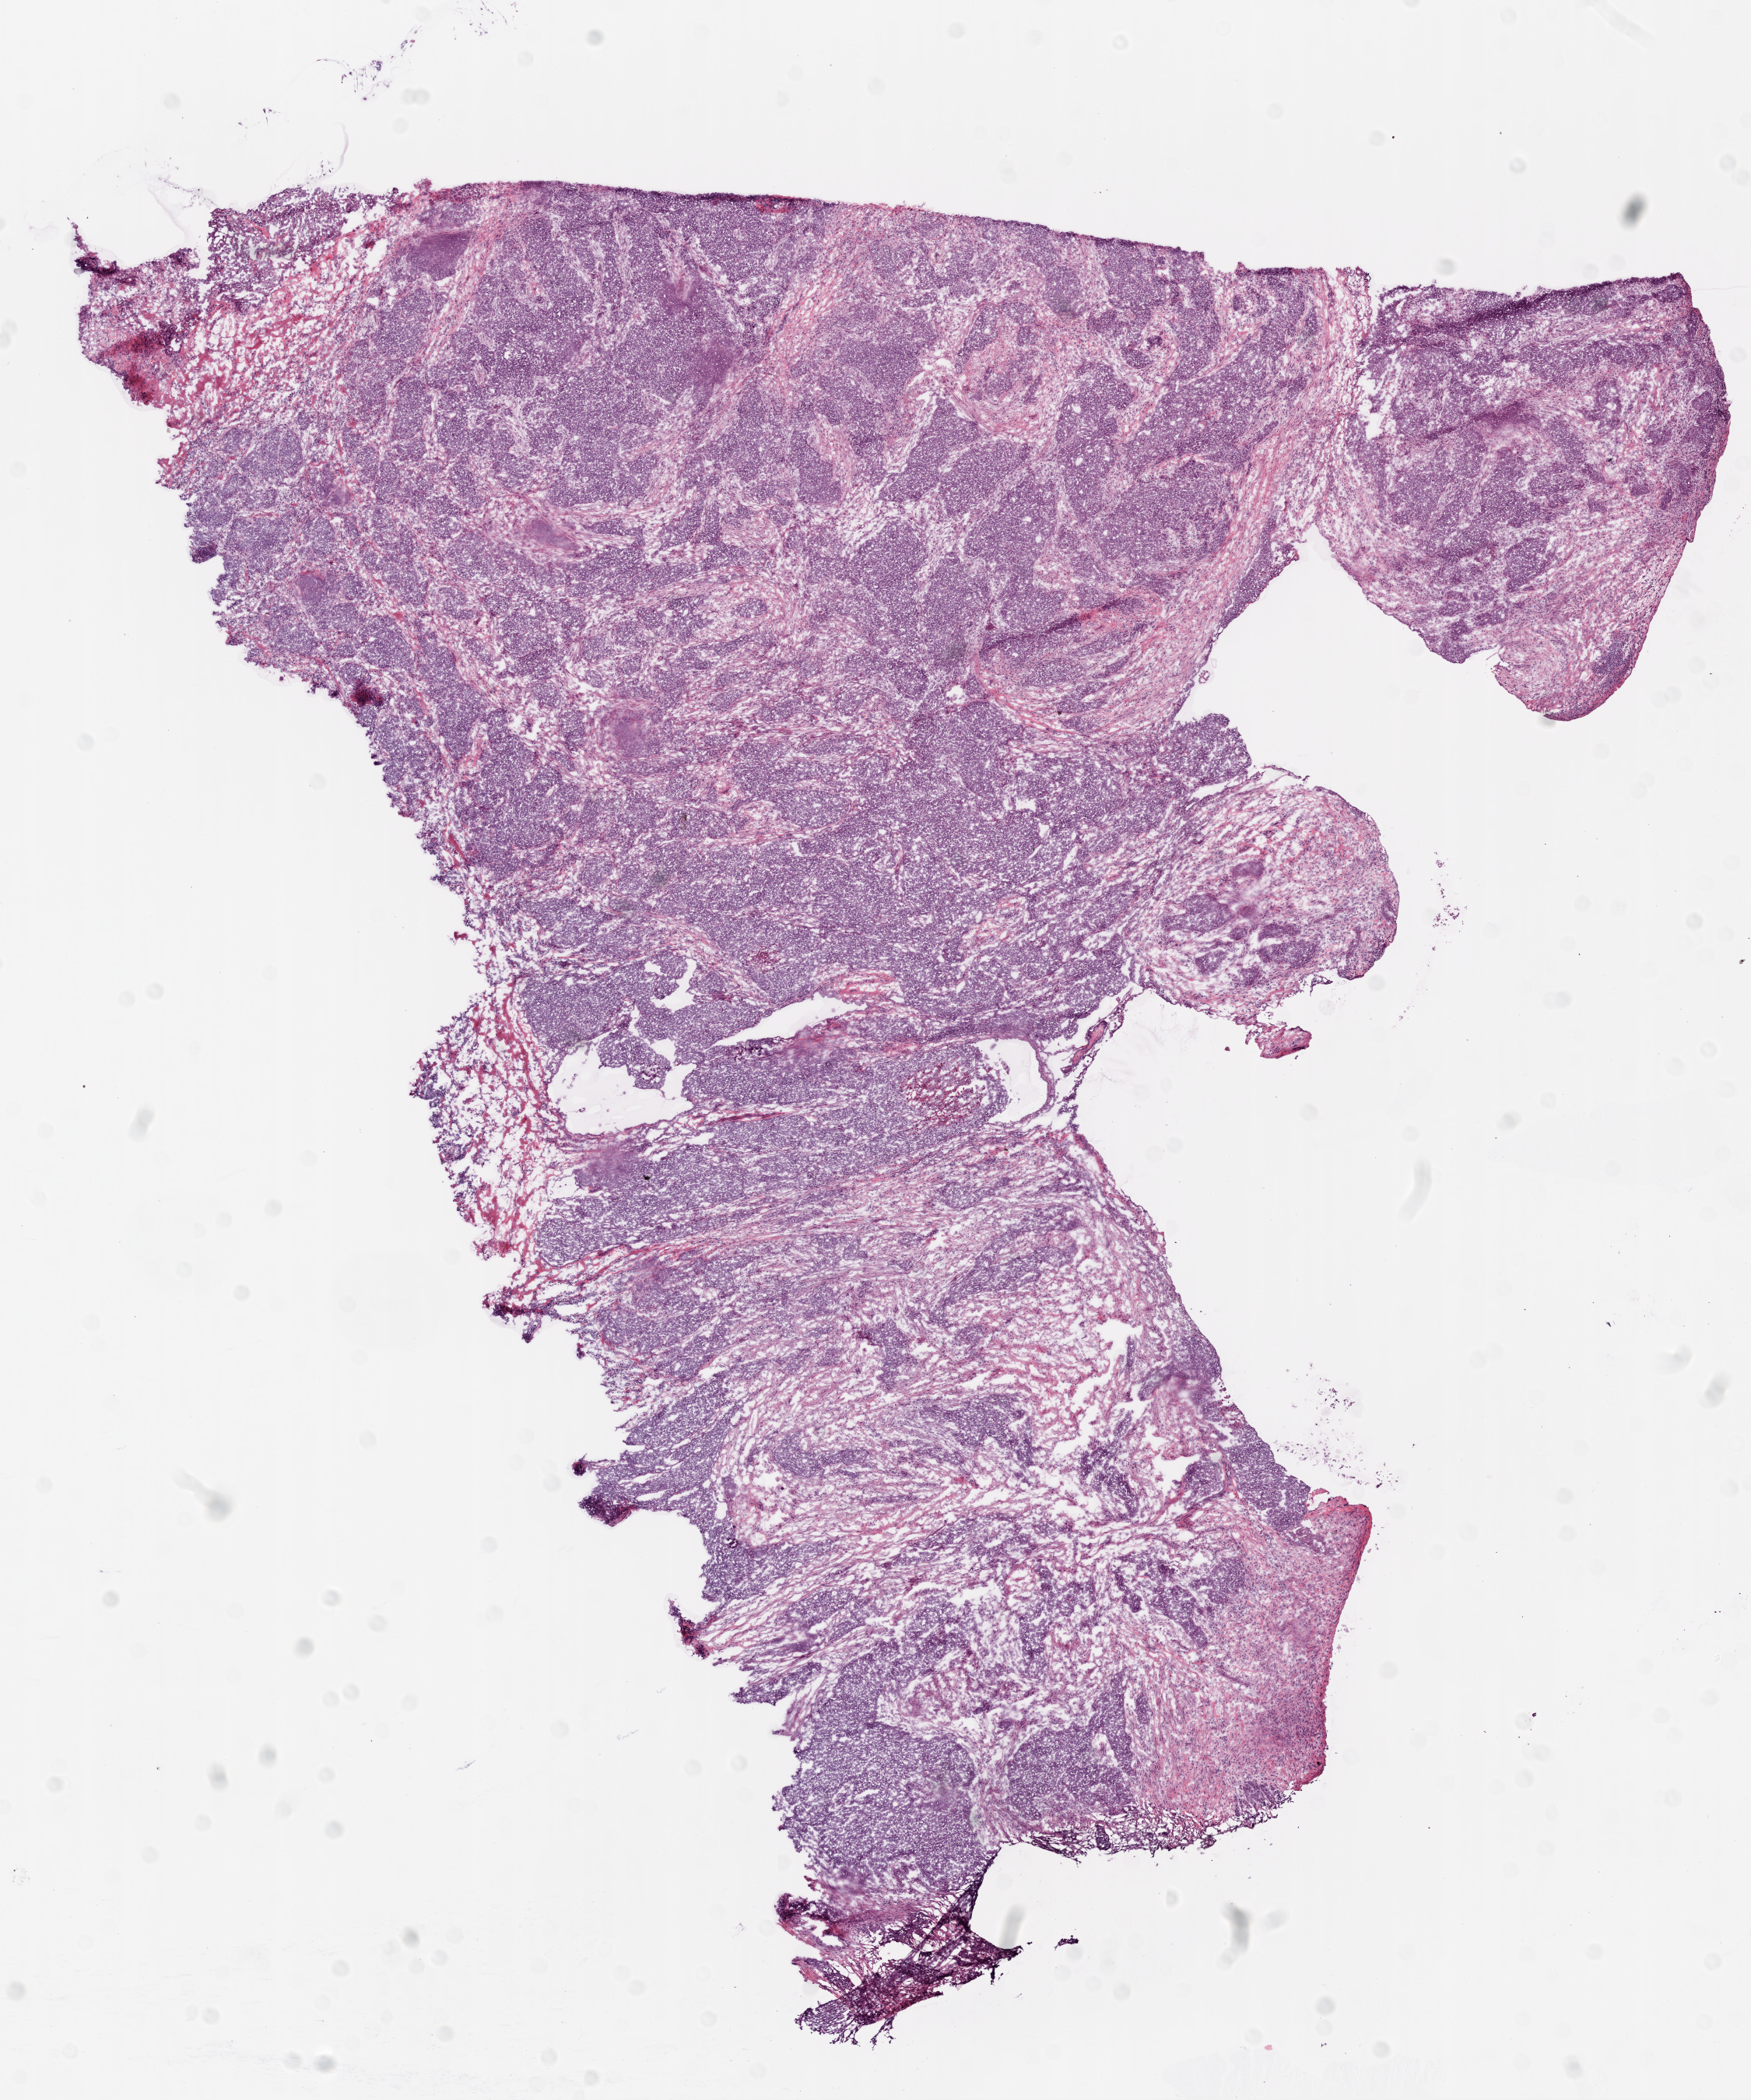
H&E-stained whole-slide image — whole scanned area (about 9.0 x 10.8 mm, acquisition: 20x scan) shown as a low-resolution overview. Frozen section from the top of the tissue portion. Ovary, primary tumour sample. Female patient; age at initial diagnosis 46 years. Histologic grade: G3 (poorly differentiated). Composition of this section per pathologist review: tumour cells 80%, tumour nuclei 95%, normal cells 10%, stromal cells 5%, necrosis 5%.
- laterality: bilateral
- pathologic diagnosis: Serous cystadenocarcinoma, NOS
- FIGO stage: IIIC